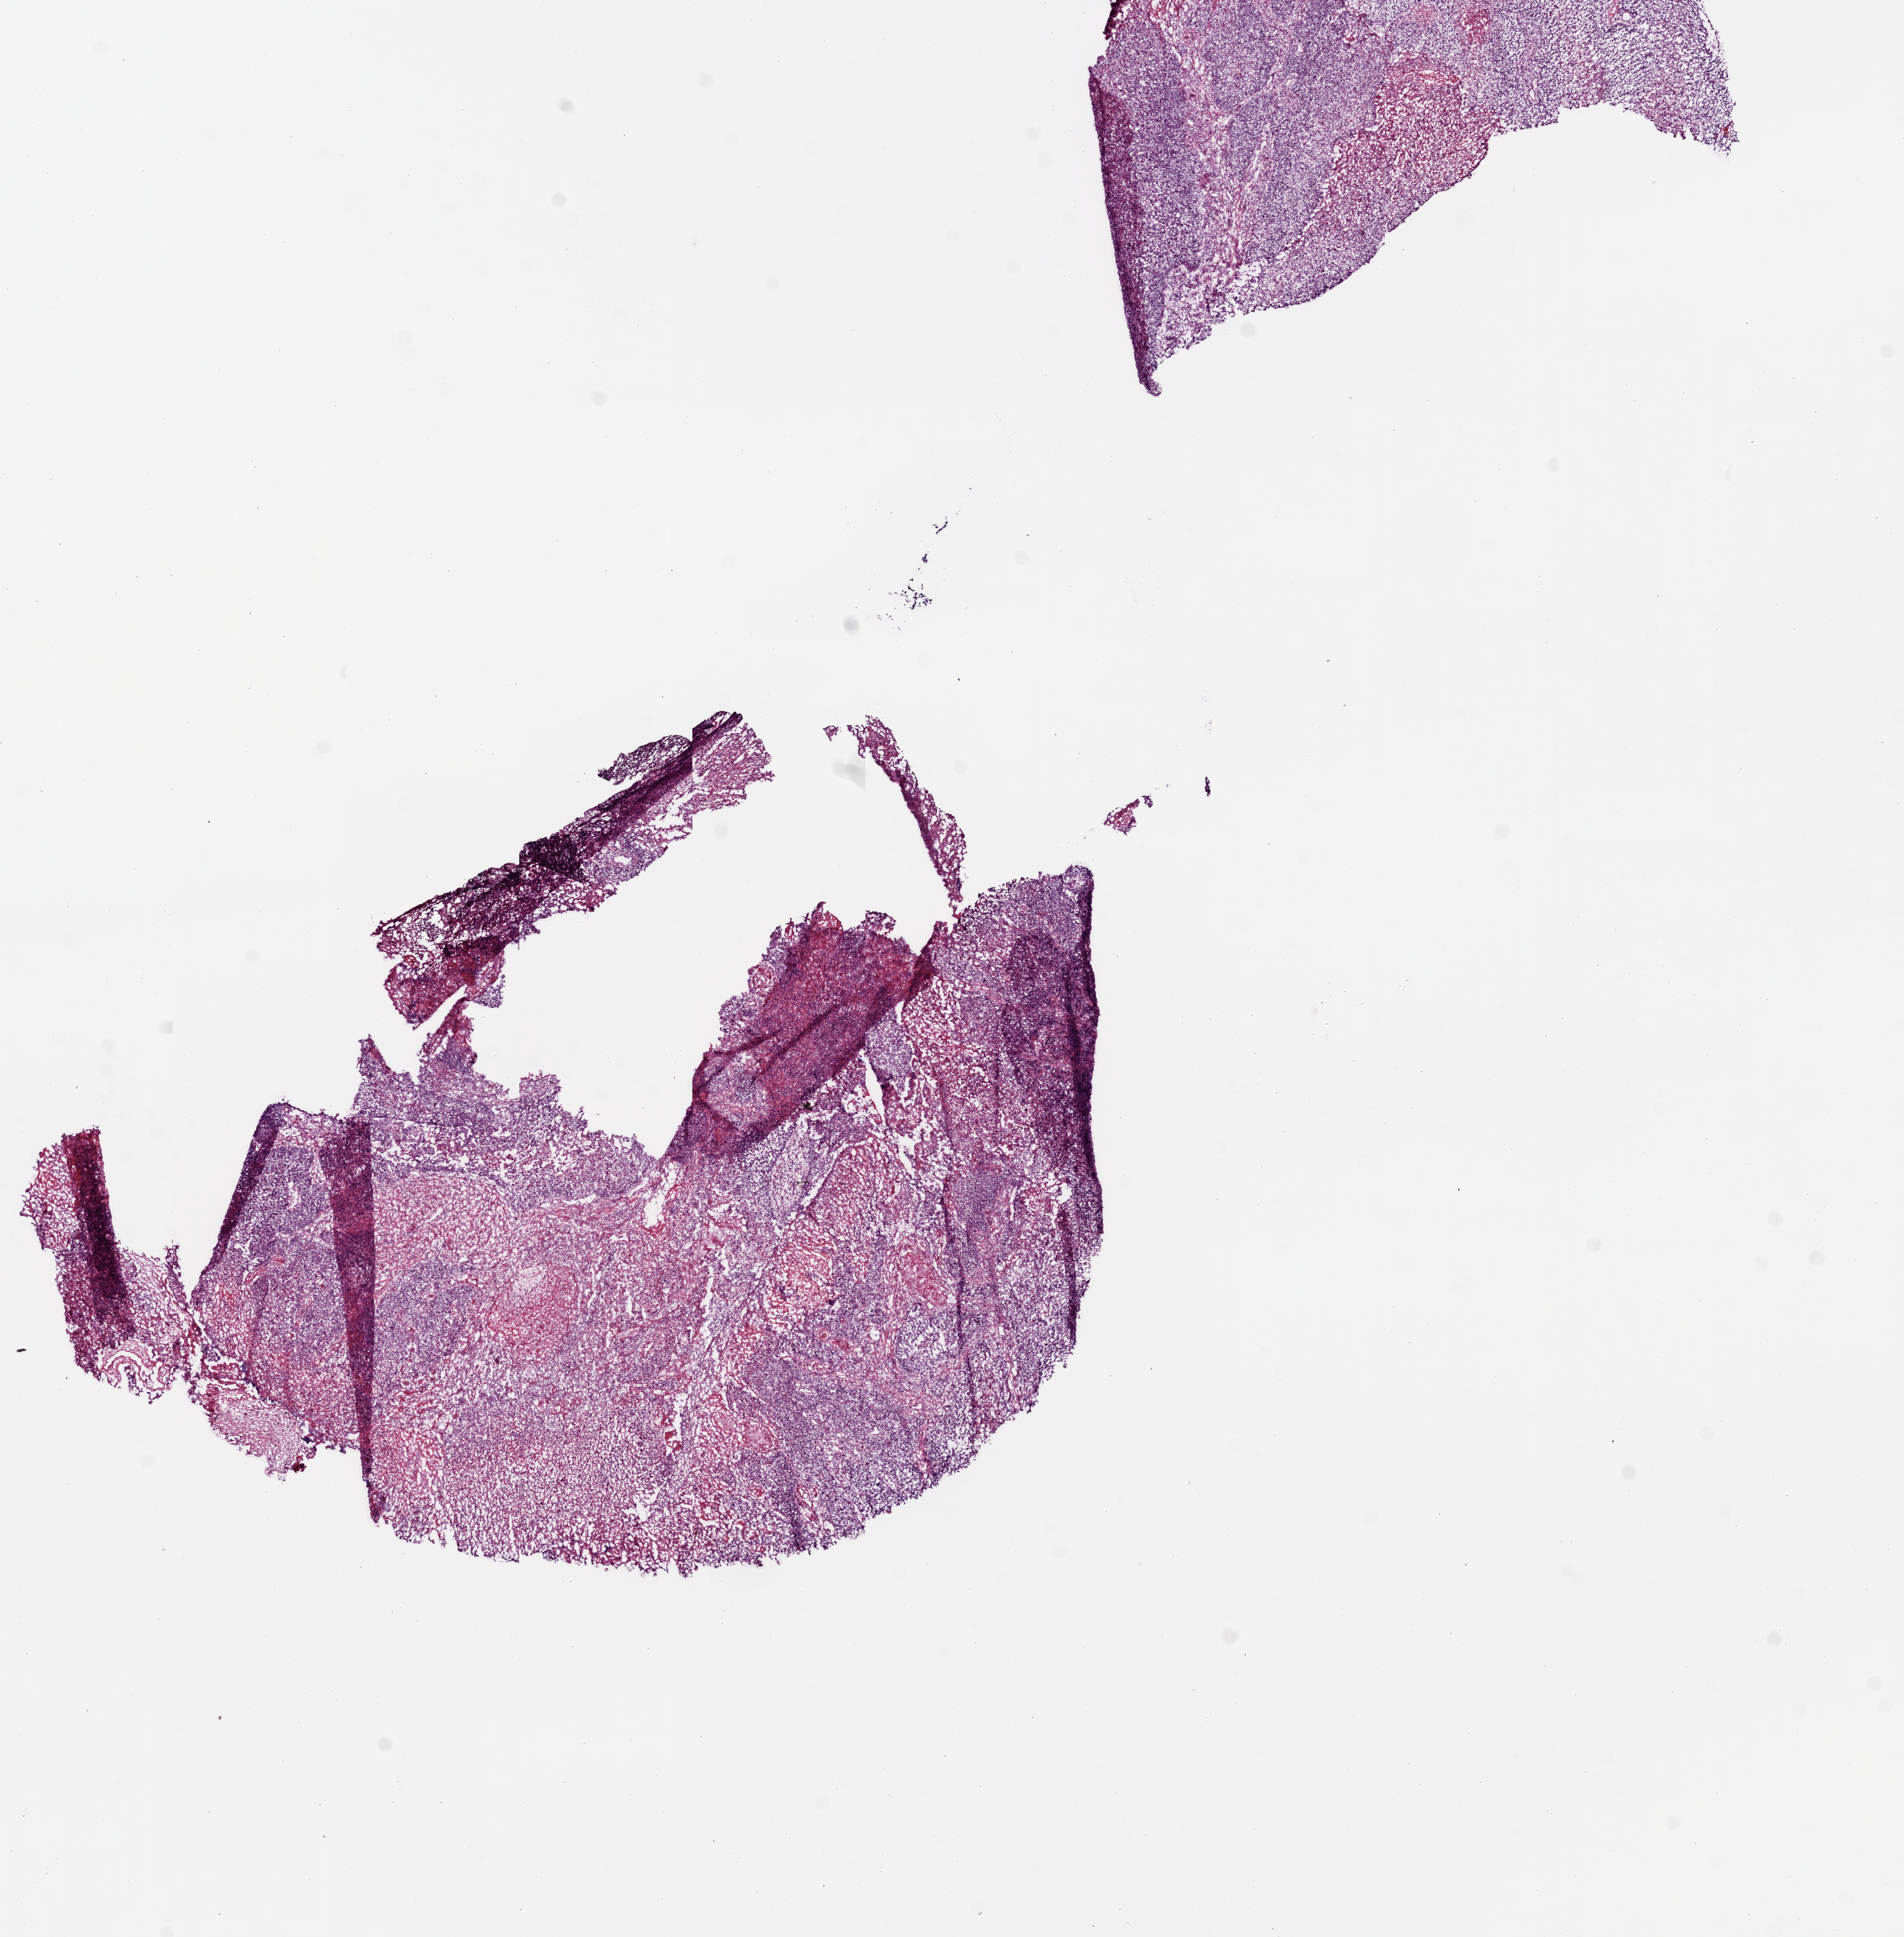
Digitized H&E tissue section (whole slide), shown as a low-resolution overview of the whole scanned area (about 11.0 x 11.2 mm, acquisition: 20x scan); frozen section; head and neck, primary tumour sample. Male, age 56 years at initial diagnosis. Histologic grade: G2 (moderately differentiated). Composition of this section per pathologist review: tumour cells 70%, tumour nuclei 75%, normal cells 0%, stromal cells 30%, necrosis 0%.
* AJCC pathologic stage: IVA (7th edition)
* histologic diagnosis: Squamous cell carcinoma, NOS (larynx, NOS)